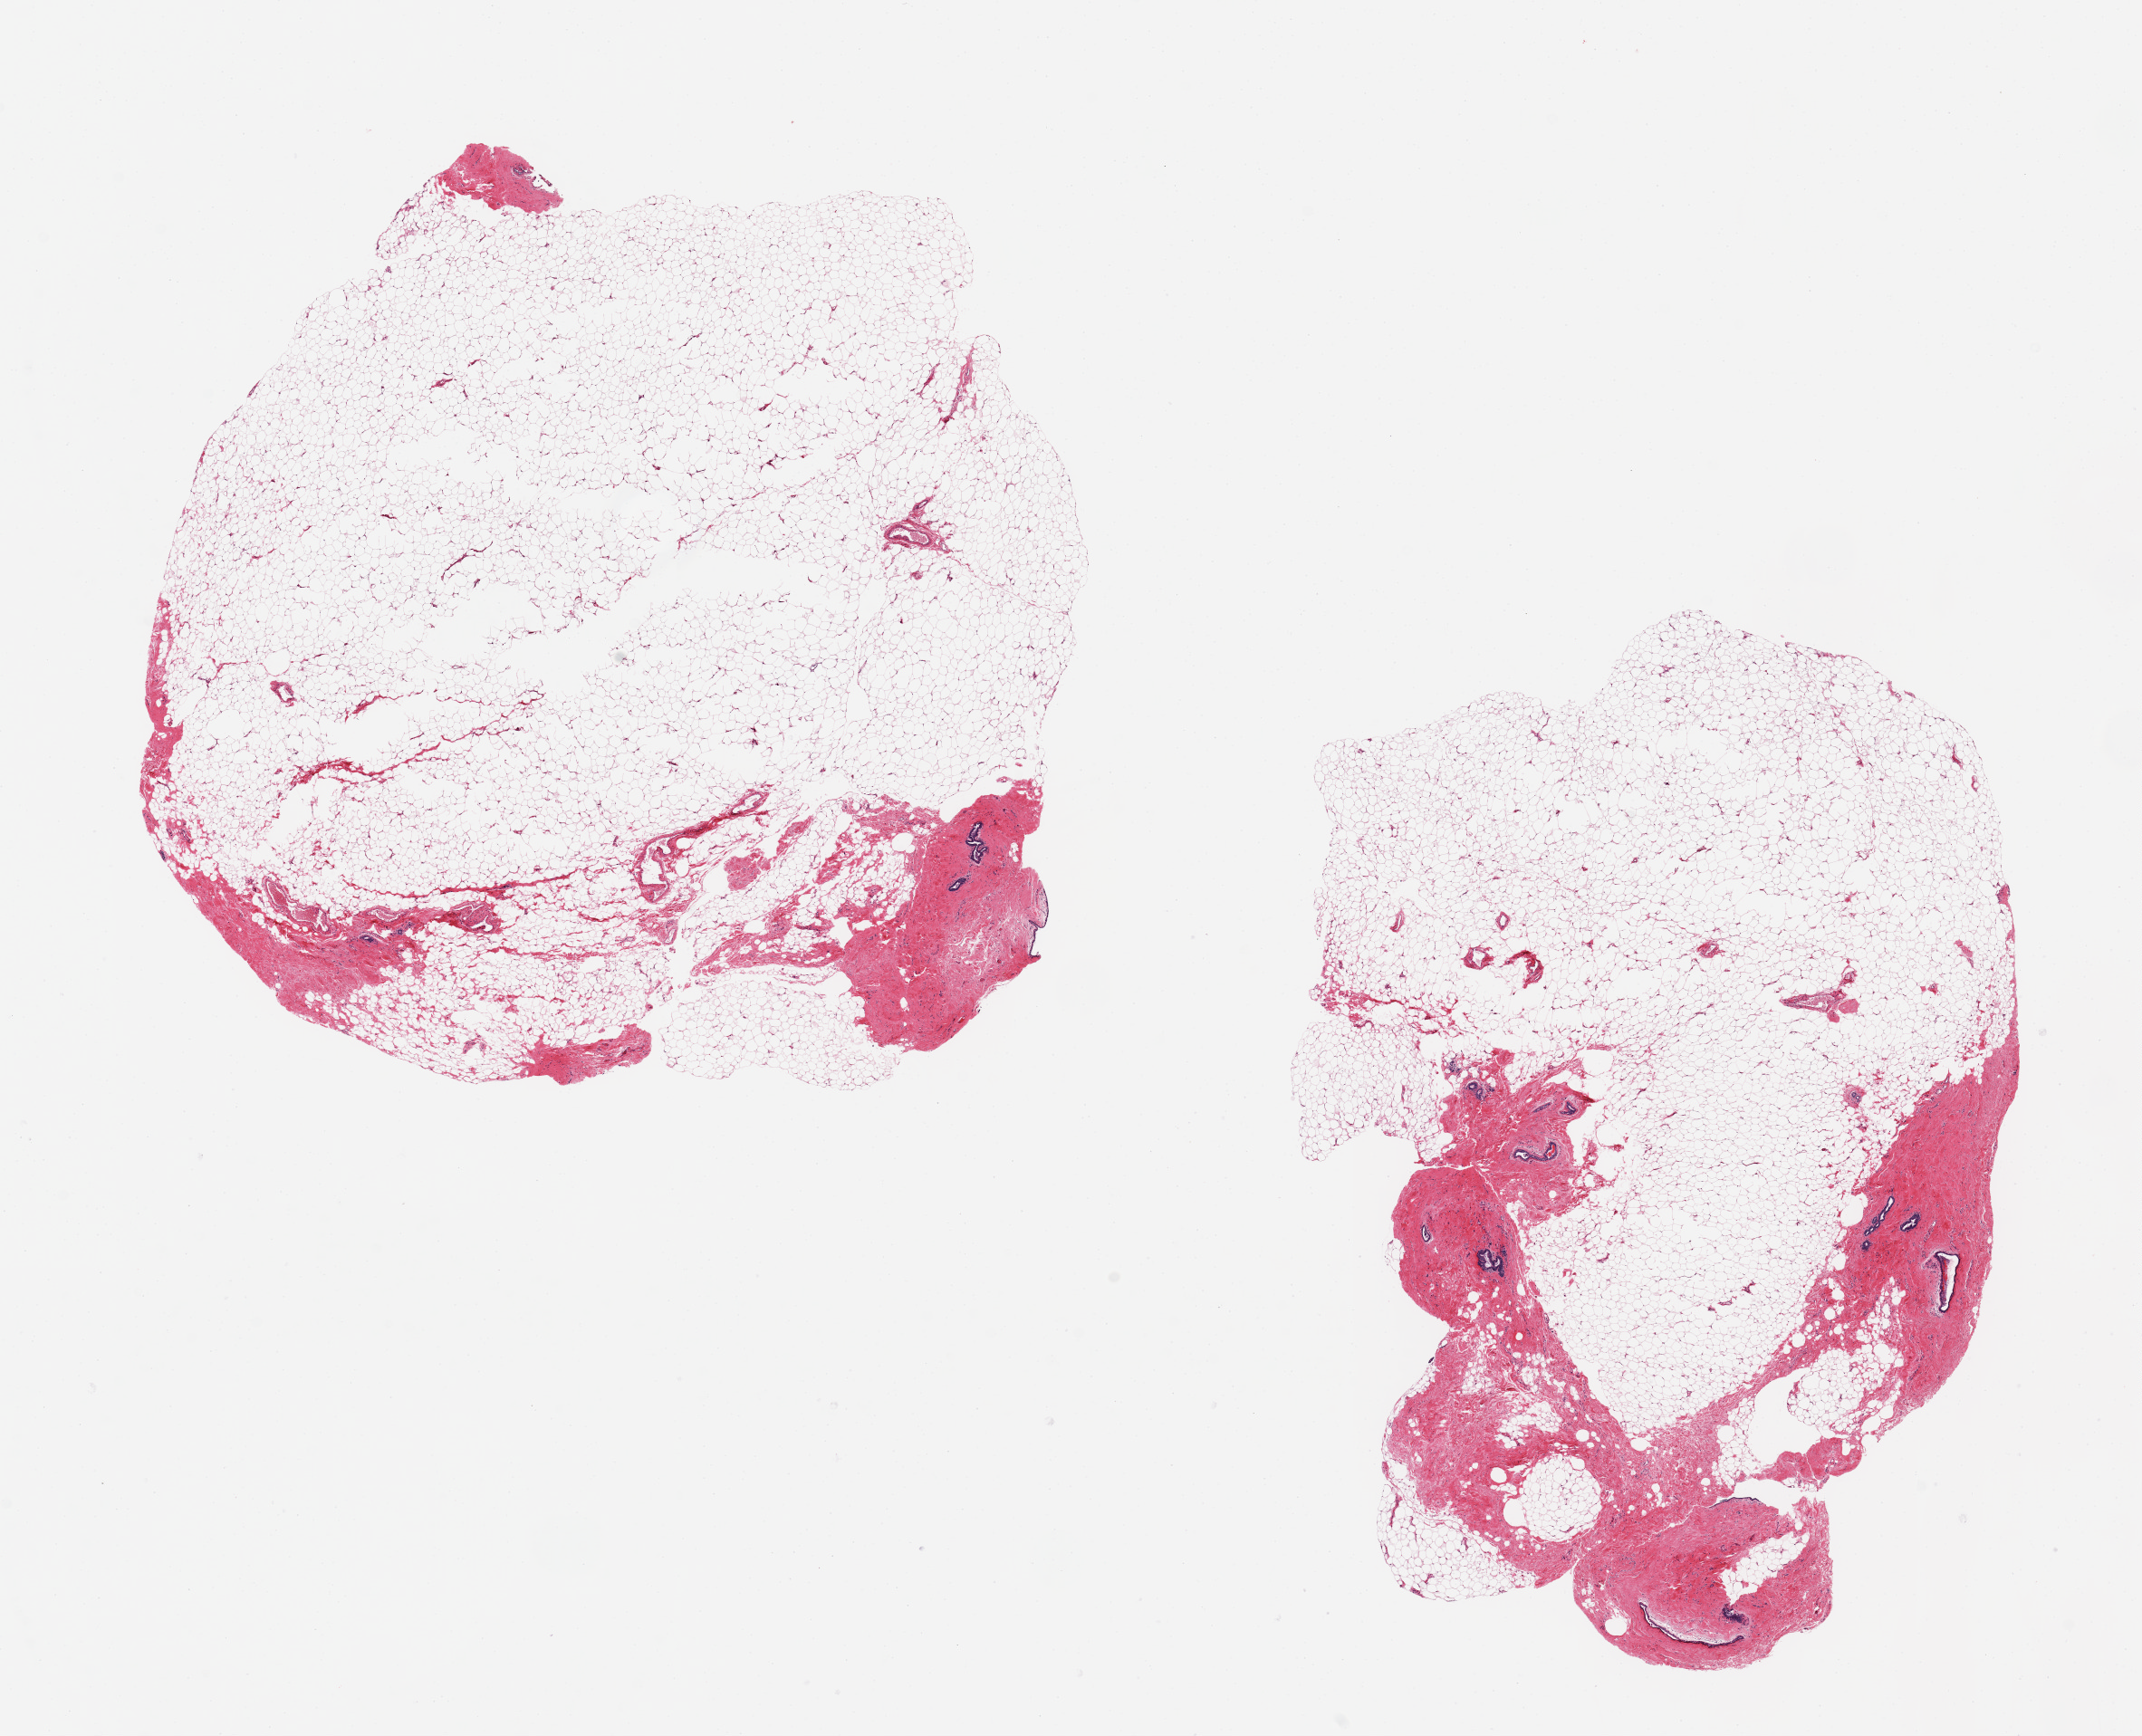
H&E whole-slide image, shown as a low-resolution overview of the whole scanned area (about 18.7 x 15.2 mm, acquisition: 20x scan). PAXgene-fixed, paraffin-embedded tissue. Sampled site (target tissue): breast. Tissue donor sample. Donor: female.
Review note (as recorded): 2 pieces, 8x8 & 9x6 mm; atrophic; 70 & 90 % adipose.